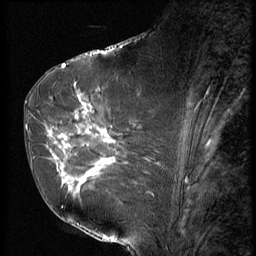
Breast MRI (dynamic contrast-enhanced), one sagittal slice; position 32 of 56 along the scan axis; 3 images stored at this slice position (order not interpretable as contrast timing); 1.5 T; TE 4.2 ms, TR 9 ms; 2.5 mm slice thickness; 256 × 256 image matrix, field of view 180 × 180 mm. Female patient, age 61 years. From the clinical record (not read from this slice): setting: breast cancer imaged before/during neoadjuvant chemotherapy; receptor status: HR-positive, HER2-negative.
Structures marked on this image (semi-automatic segmentation, software-assisted and operator-edited):
- analysis volume of interest (the breast-tissue region the enhancement analysis was run in; not a lesion): bounding box [x1, y1, x2, y2] px = [47, 89, 153, 191]
- tumour enhancement mask (voxels above the 140 % enhancement threshold inside the analysis volume of interest): [48, 95, 116, 184]